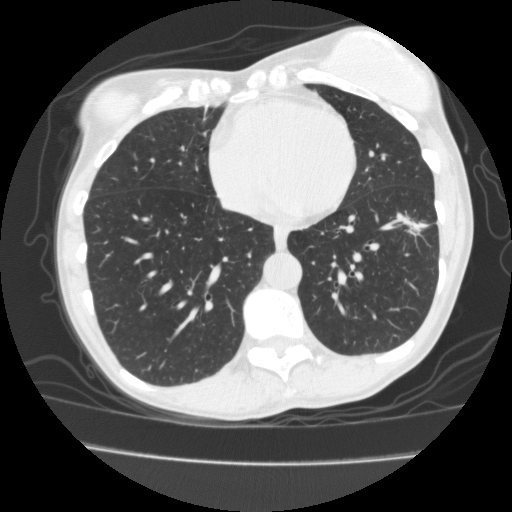
Low-dose screening chest CT, one axial slice; position 59 of 171 along the scan axis; 120 kVp; lung window (W 1500 / L -600 HU); 2 mm slice thickness; 512 × 512 image matrix.
Outlined on this slice (manually delineated by an expert):
- lesion 1 (tumor, lower lobe of left lung): bounding box [x1, y1, x2, y2] px = [405, 218, 424, 232]